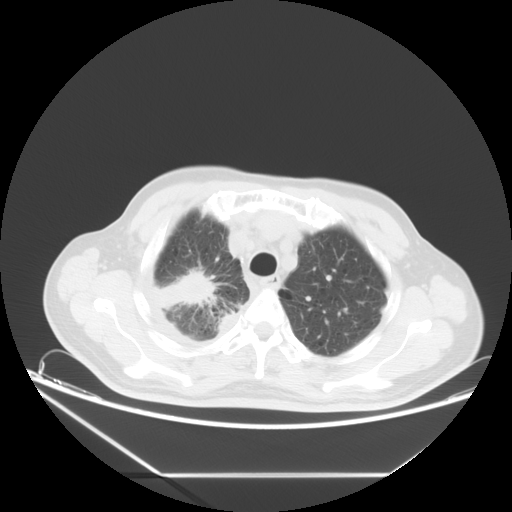
Chest CT, one axial slice. Slice 14 of 16 in the series (ordered by position). Lung window (W 1500 / L -600 HU). 5 mm slice thickness. 512 × 512 image matrix. Patient: male, 75 years. From the clinical record (not read from this slice): clinical TNM (as recorded): T1c N1 M1.
Structures marked on this image (bounding box drawn by a radiologist):
- lung tumour (recorded histology: adenocarcinoma): box from (x=150, y=270) to (x=219, y=317) px